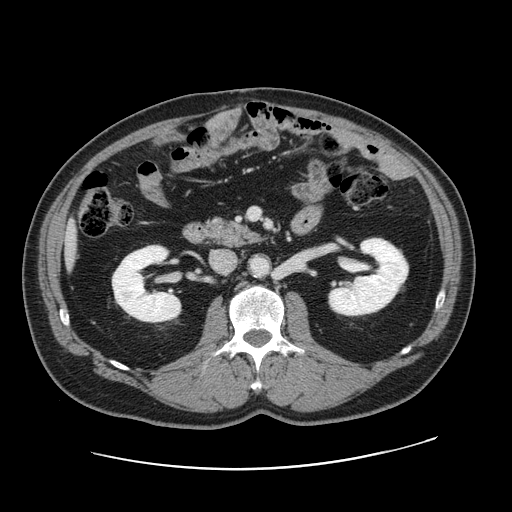
Contrast-enhanced abdominal CT, one axial slice. Slice 62 of 178 in the series (ordered by position). Intravenous contrast given. Soft-tissue window (W 400 / L 40 HU). 512 × 512 image matrix, field of view 403 × 403 mm. Male patient, age 63 years. Case-level facts recorded for this patient, not image findings: diagnosis: colorectal cancer liver metastases, imaged before liver resection; multiple liver metastases: yes; largest metastasis: 8 cm.
Structures marked on this image (manually delineated by an expert):
- liver: bounding box [x1, y1, x2, y2] px = [66, 231, 75, 254]